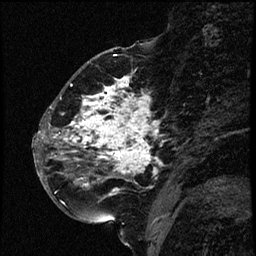
Breast MRI (dynamic contrast-enhanced), one sagittal slice; slice 27 of 66 in the series (ordered by position); dynamic contrast-enhanced study with each time point stored as its own series, time point 2 of 3 at this slice position (early post-contrast, ordered by acquisition time); 1.5 T; TE 4.2 ms, TR 17.6 ms; 2 mm slice thickness; 256 × 256 image matrix, field of view 200 × 200 mm. Female patient. Case-level facts recorded for this patient, not image findings: setting: breast cancer imaged before/during neoadjuvant chemotherapy; receptor status: HER2-positive.
Outlined on this slice (semi-automatically segmented with operator editing):
- analysis volume of interest (the breast-tissue region the enhancement analysis was run in; not a lesion): bounding box <52,69,173,209> (left, top, right, bottom; pixels)
- tumour enhancement mask (voxels above the 100 % enhancement threshold inside the analysis volume of interest): <53,77,161,195>